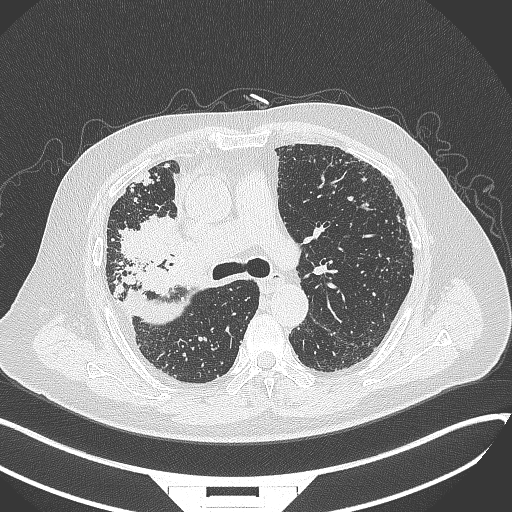
Chest CT, one axial slice. Slice 219 of 384 in the series (ordered by position). Reconstruction kernel B70f. 120 kVp. Lung window (W 1500 / L -600 HU). 1 mm slice thickness. 512 × 512 image matrix, field of view 400 × 400 mm. Male patient, age 69 years. Case-level facts recorded for this patient, not image findings: clinical TNM (as recorded): T4 N3 M1.
Structures marked on this image (bounding box drawn by a radiologist):
- lung tumour (recorded histology: adenocarcinoma): box from (x=115, y=216) to (x=176, y=270) px